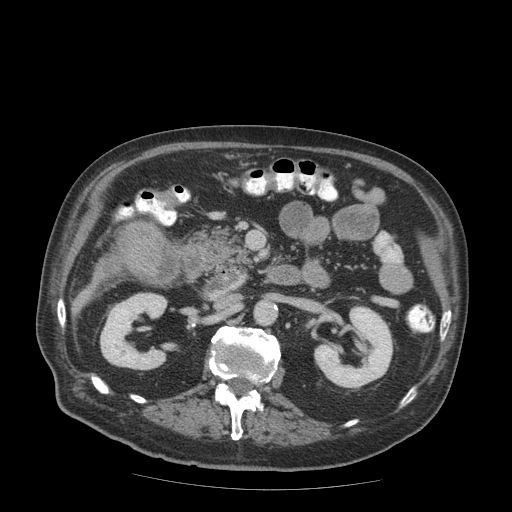
Contrast-enhanced abdominal CT (liver protocol), one axial slice; slice 23 of 99 in the series (ordered by position); soft-tissue window (W 400 / L 40 HU); 2.5 mm slice thickness; 512 × 512 image matrix, field of view 420 × 420 mm. From the clinical record (not read from this slice): diagnosis: hepatocellular carcinoma (patient treated with transarterial chemoembolisation; whether this scan precedes or follows treatment is not stated here); TNM stage (as recorded): Stage-IIIB; Child-Pugh class: A; tumour nodularity: multinodular.
Outlined on this slice (semi-automatically segmented with operator editing):
- mass: box from (x=118, y=223) to (x=157, y=268) px